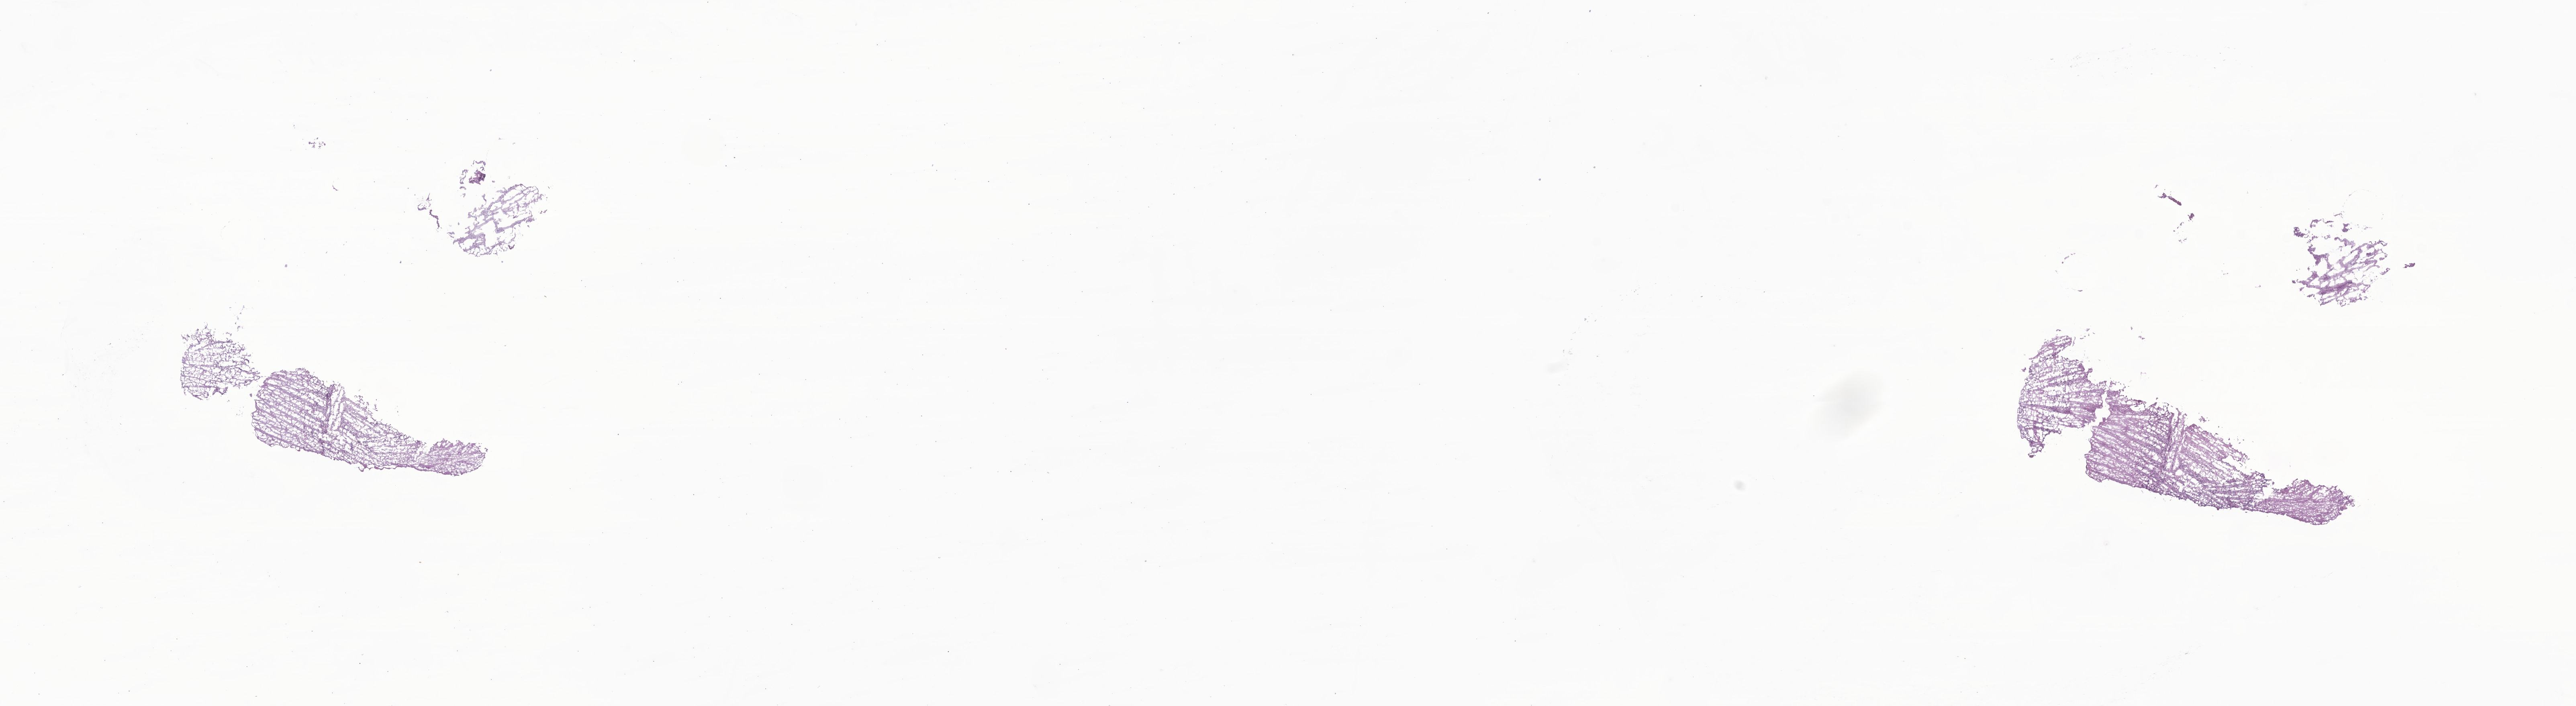
Whole-slide image, H&E stain of tumor tissue from the brain — shown as a low-resolution overview of the whole scanned area (about 27.0 x 7.4 mm). Frozen section. Patient female; age 102 months (8 years 6 months).
Recorded diagnosis: Neoplasm, uncertain whether benign or malignant.